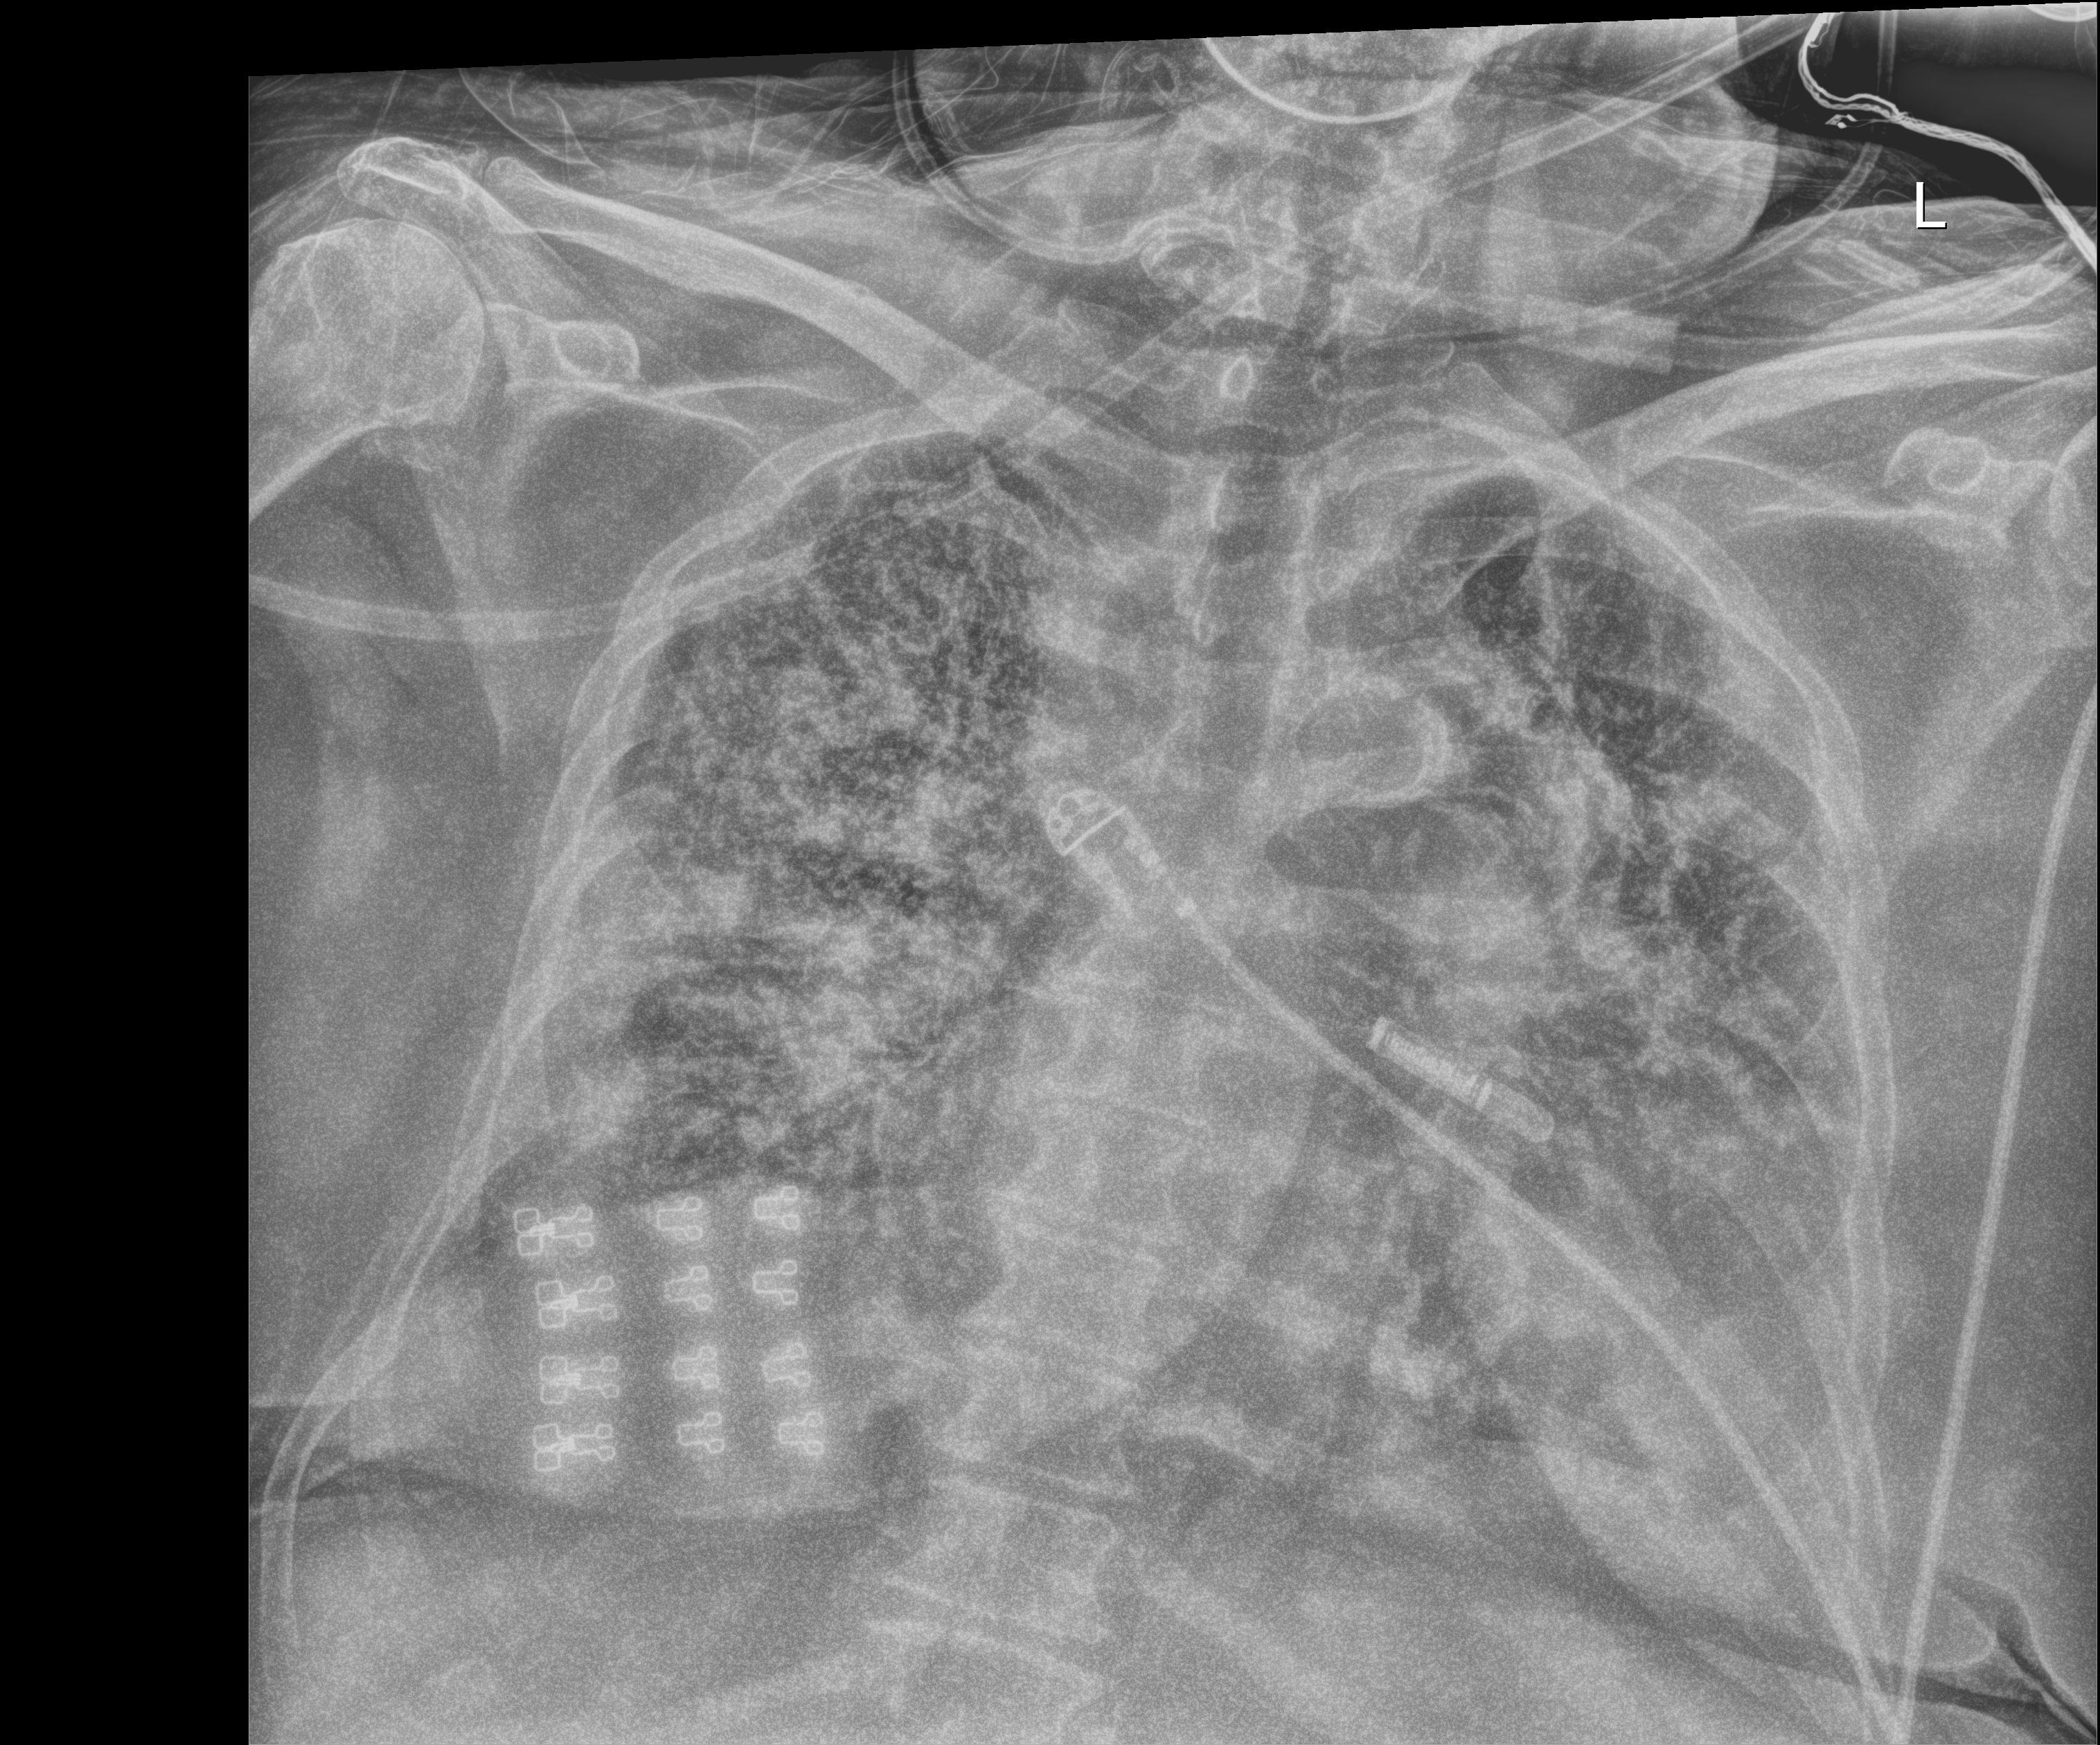
Portable chest radiograph; anteroposterior (AP) projection. Patient hospitalised with COVID-19; female, aged 60–74 years.
From the hospital-stay record, not from the radiograph (when in the stay this image was taken is not recorded):
- diabetes (admission record): yes
- mechanically ventilated during this hospital stay: yes
- length of hospital stay: 28 days